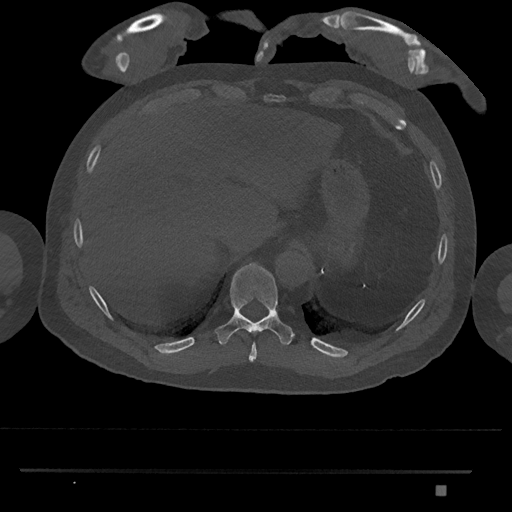
CT including the spine, one axial slice; slice 1005 of 1134 in the series (ordered by position); reconstruction kernel Br40s/3; bone window (W 1800 / L 400 HU); 512 × 512 image matrix, field of view 429 × 429 mm. Male patient, age 65 years. Case-level facts recorded for this patient, not image findings: primary cancer: prostate.
Annotated regions visible in this slice (semi-automatically segmented with operator editing):
- T10 vertebra: bounding box <215,262,294,345> (left, top, right, bottom; pixels)
- T9 vertebra: <248,343,257,362>